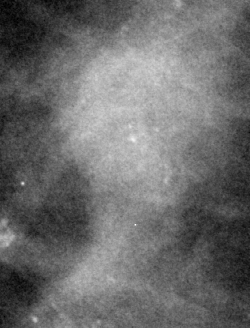
Region of interest cut from a scanned film mammogram (one marked finding); right breast; CC view.
- Mass, shape irregular, margins spiculated; BI-RADS assessment category 5; pathology result (as recorded, not read from the image): malignant.